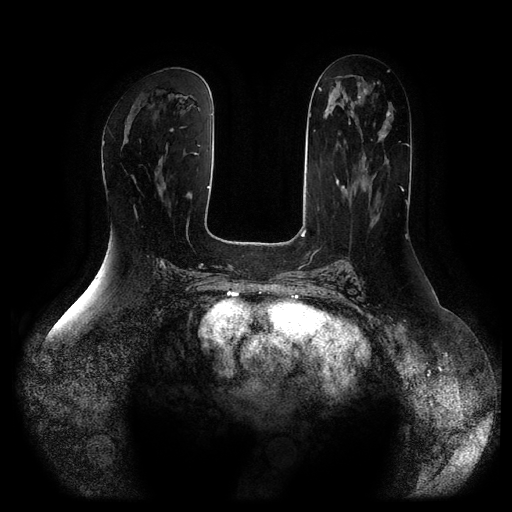
Breast MRI (dynamic contrast-enhanced, multi-phase), one axial slice. Position 44 of 116 along the scan axis. Dynamic contrast-enhanced series, time point 2 of 5 at this slice position (early post-contrast). 1.5 T. TE 2.5 ms, TR 5.2 ms. 2 mm slice thickness. 512 × 512 image matrix. Female patient, age 66 years.
Annotated regions visible in this slice (semi-automatic segmentation, software-assisted and operator-edited):
- breast lesion (labelled 'tumour' in the annotation; benign lesions carry a separate 'benign' label): bounding box (x1, y1, x2, y2) in pixels: (169, 128, 174, 132)